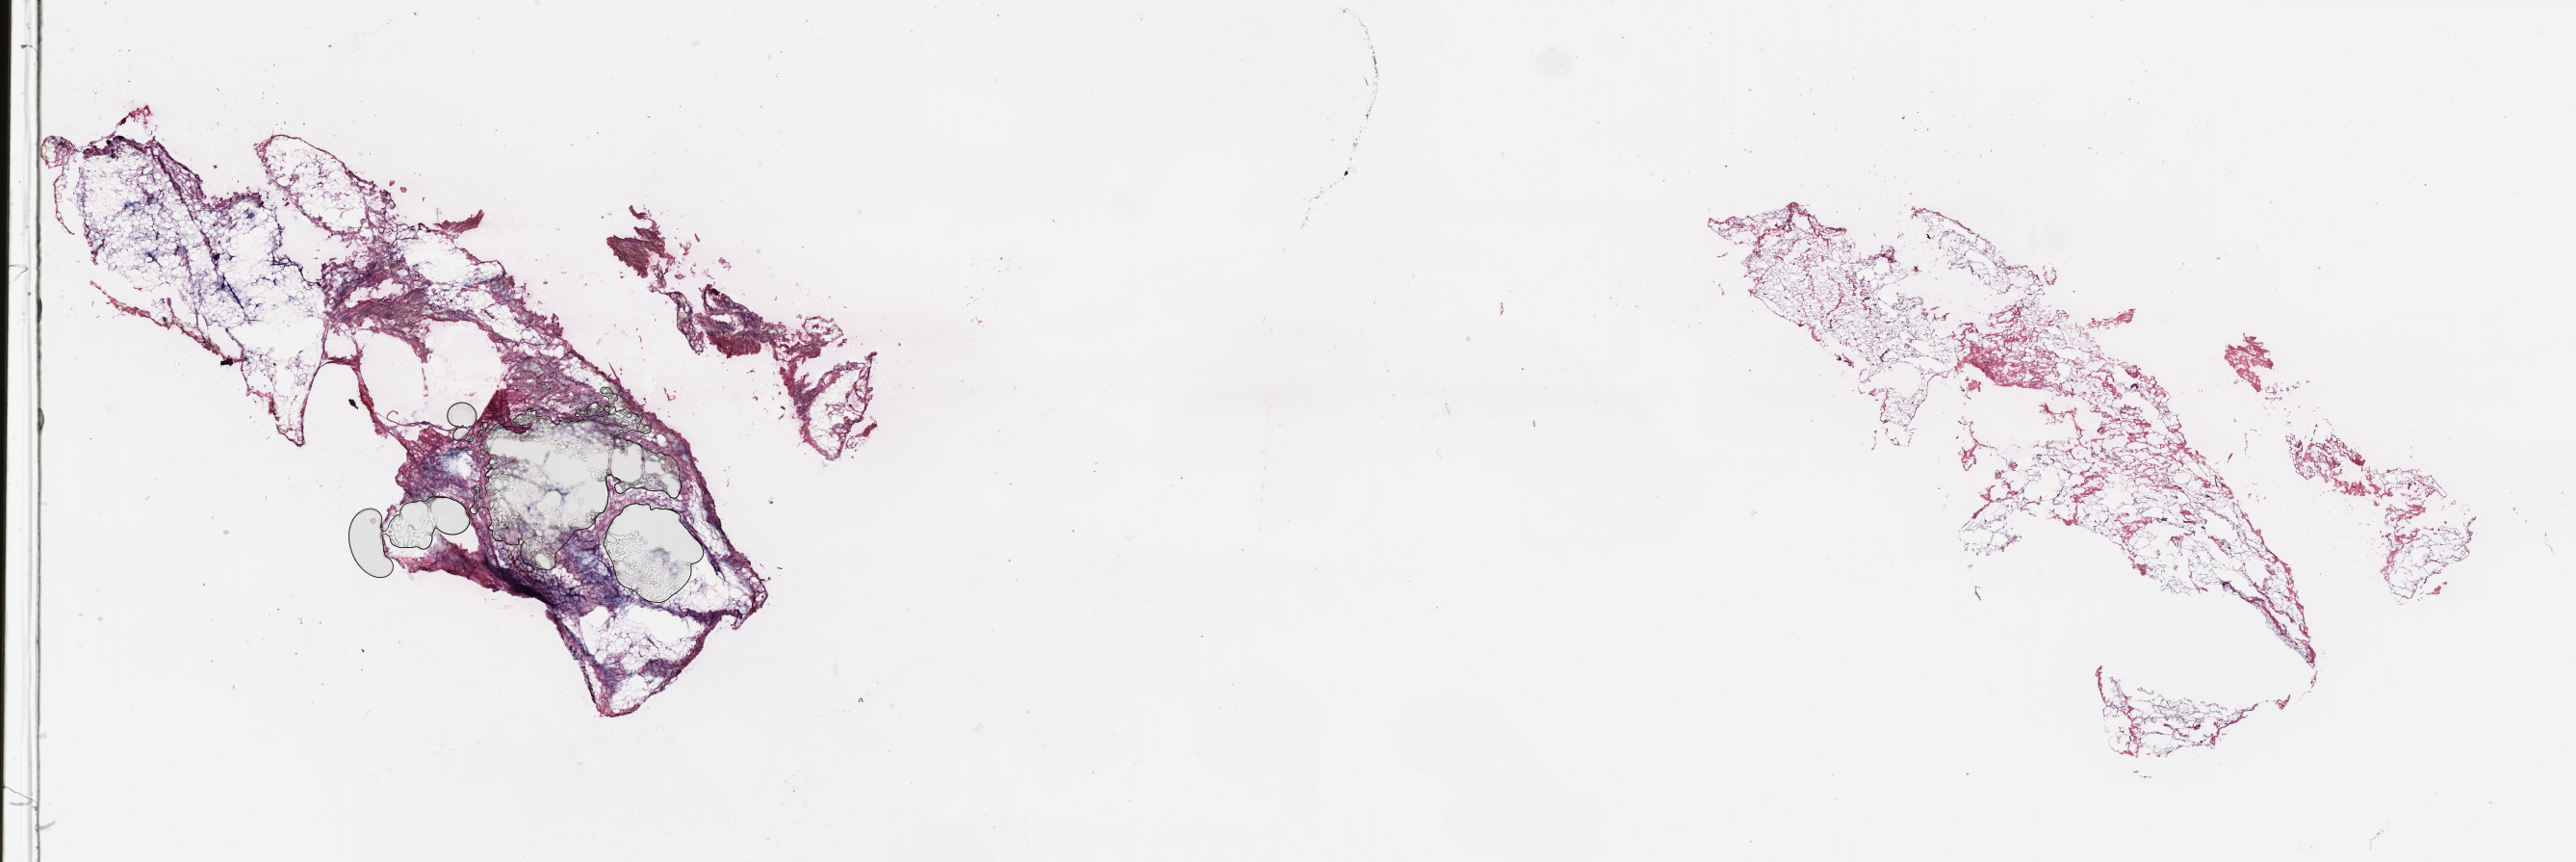
H&E whole-slide image — whole scanned area (about 42.3 x 14.2 mm) shown as a low-resolution overview, breast, tissue type not recorded.
* patient diagnosis (cohort enrolment): breast cancer (breast)